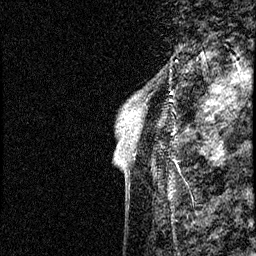
Breast MRI (dynamic contrast-enhanced), one sagittal slice. Dynamic contrast-enhanced study with each time point stored as its own series, time point 2 of 4 at this slice position (early post-contrast, ordered by acquisition time). 1.5 T. TE 4.2 ms, TR 17.6 ms. 2 mm slice thickness. 256 × 256 image matrix, field of view 200 × 200 mm. Patient: female, 40 years. From the clinical record (not read from this slice): setting: breast cancer imaged before/during neoadjuvant chemotherapy; receptor status: HER2-positive.
Annotated regions visible in this slice (semi-automatically segmented with operator editing):
- analysis volume of interest (the breast-tissue region the enhancement analysis was run in; not a lesion): bounding box <109,55,184,206> (left, top, right, bottom; pixels)
- tumour enhancement mask (voxels above the 100 % enhancement threshold inside the analysis volume of interest): <126,113,133,119>